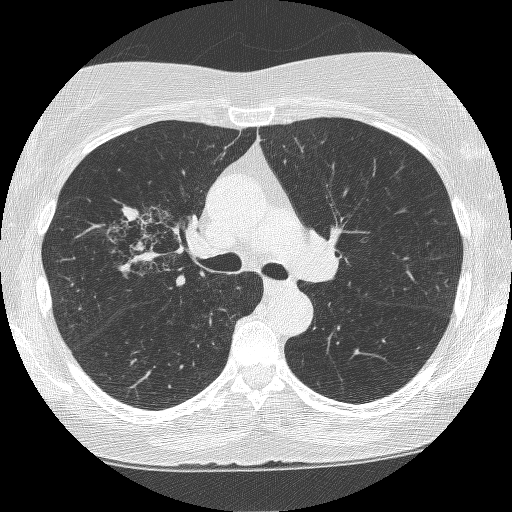
Low-dose screening chest CT, axial slice. Second annual screen. Lung window (W 1500 / L -600 HU). Lung (sharp) reconstruction kernel (BONE). Slice 155 of 249 in the series. Female participant, aged 64 years at enrolment.
Expert reader's lesion annotation, bounding box <115,205,206,291> (left, top, right, bottom; pixels). The screening reader recorded 4 non-calcified nodules or masses ≥4 mm on this exam (right upper lobe, right upper lobe, right upper lobe, left upper lobe); which of them this box marks is not recorded. Participant outcome: lung cancer diagnosed 381 days after this screen (after the third annual screen) — adenocarcinoma, NOS, right upper lobe, right middle lobe, right hilum, stage IV (AJCC 6th edition), 85 mm at pathology.